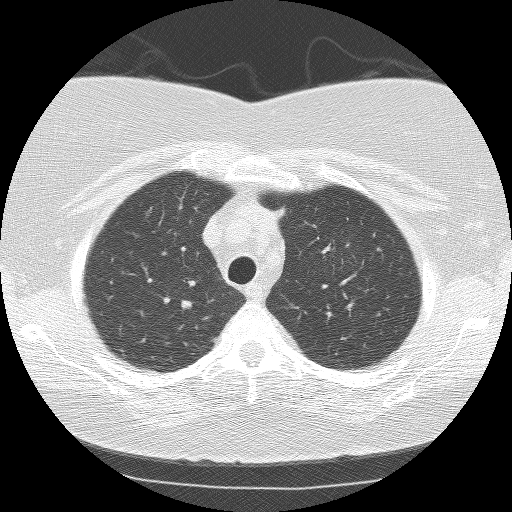
Low-dose screening chest CT, axial slice. Baseline annual screen. Lung window (W 1500 / L -600 HU). Lung (sharp) reconstruction kernel (BONE). 512 × 512 image matrix, field of view 299 × 299 mm. Female participant, aged 64 years at enrolment.
Lesion marked by an expert reader, bounding box <165,288,208,325> (left, top, right, bottom; pixels). The exam's reader record, not a measurement of the box and not confirmed to be the same lesion: non-calcified nodule or mass ≥4 mm, right upper lobe, 7 × 7 mm, smooth margins, soft tissue attenuation. Lung cancer was diagnosed 314 days after this screen: small cell carcinoma, NOS, right hilum, stage IV (AJCC 6th edition).